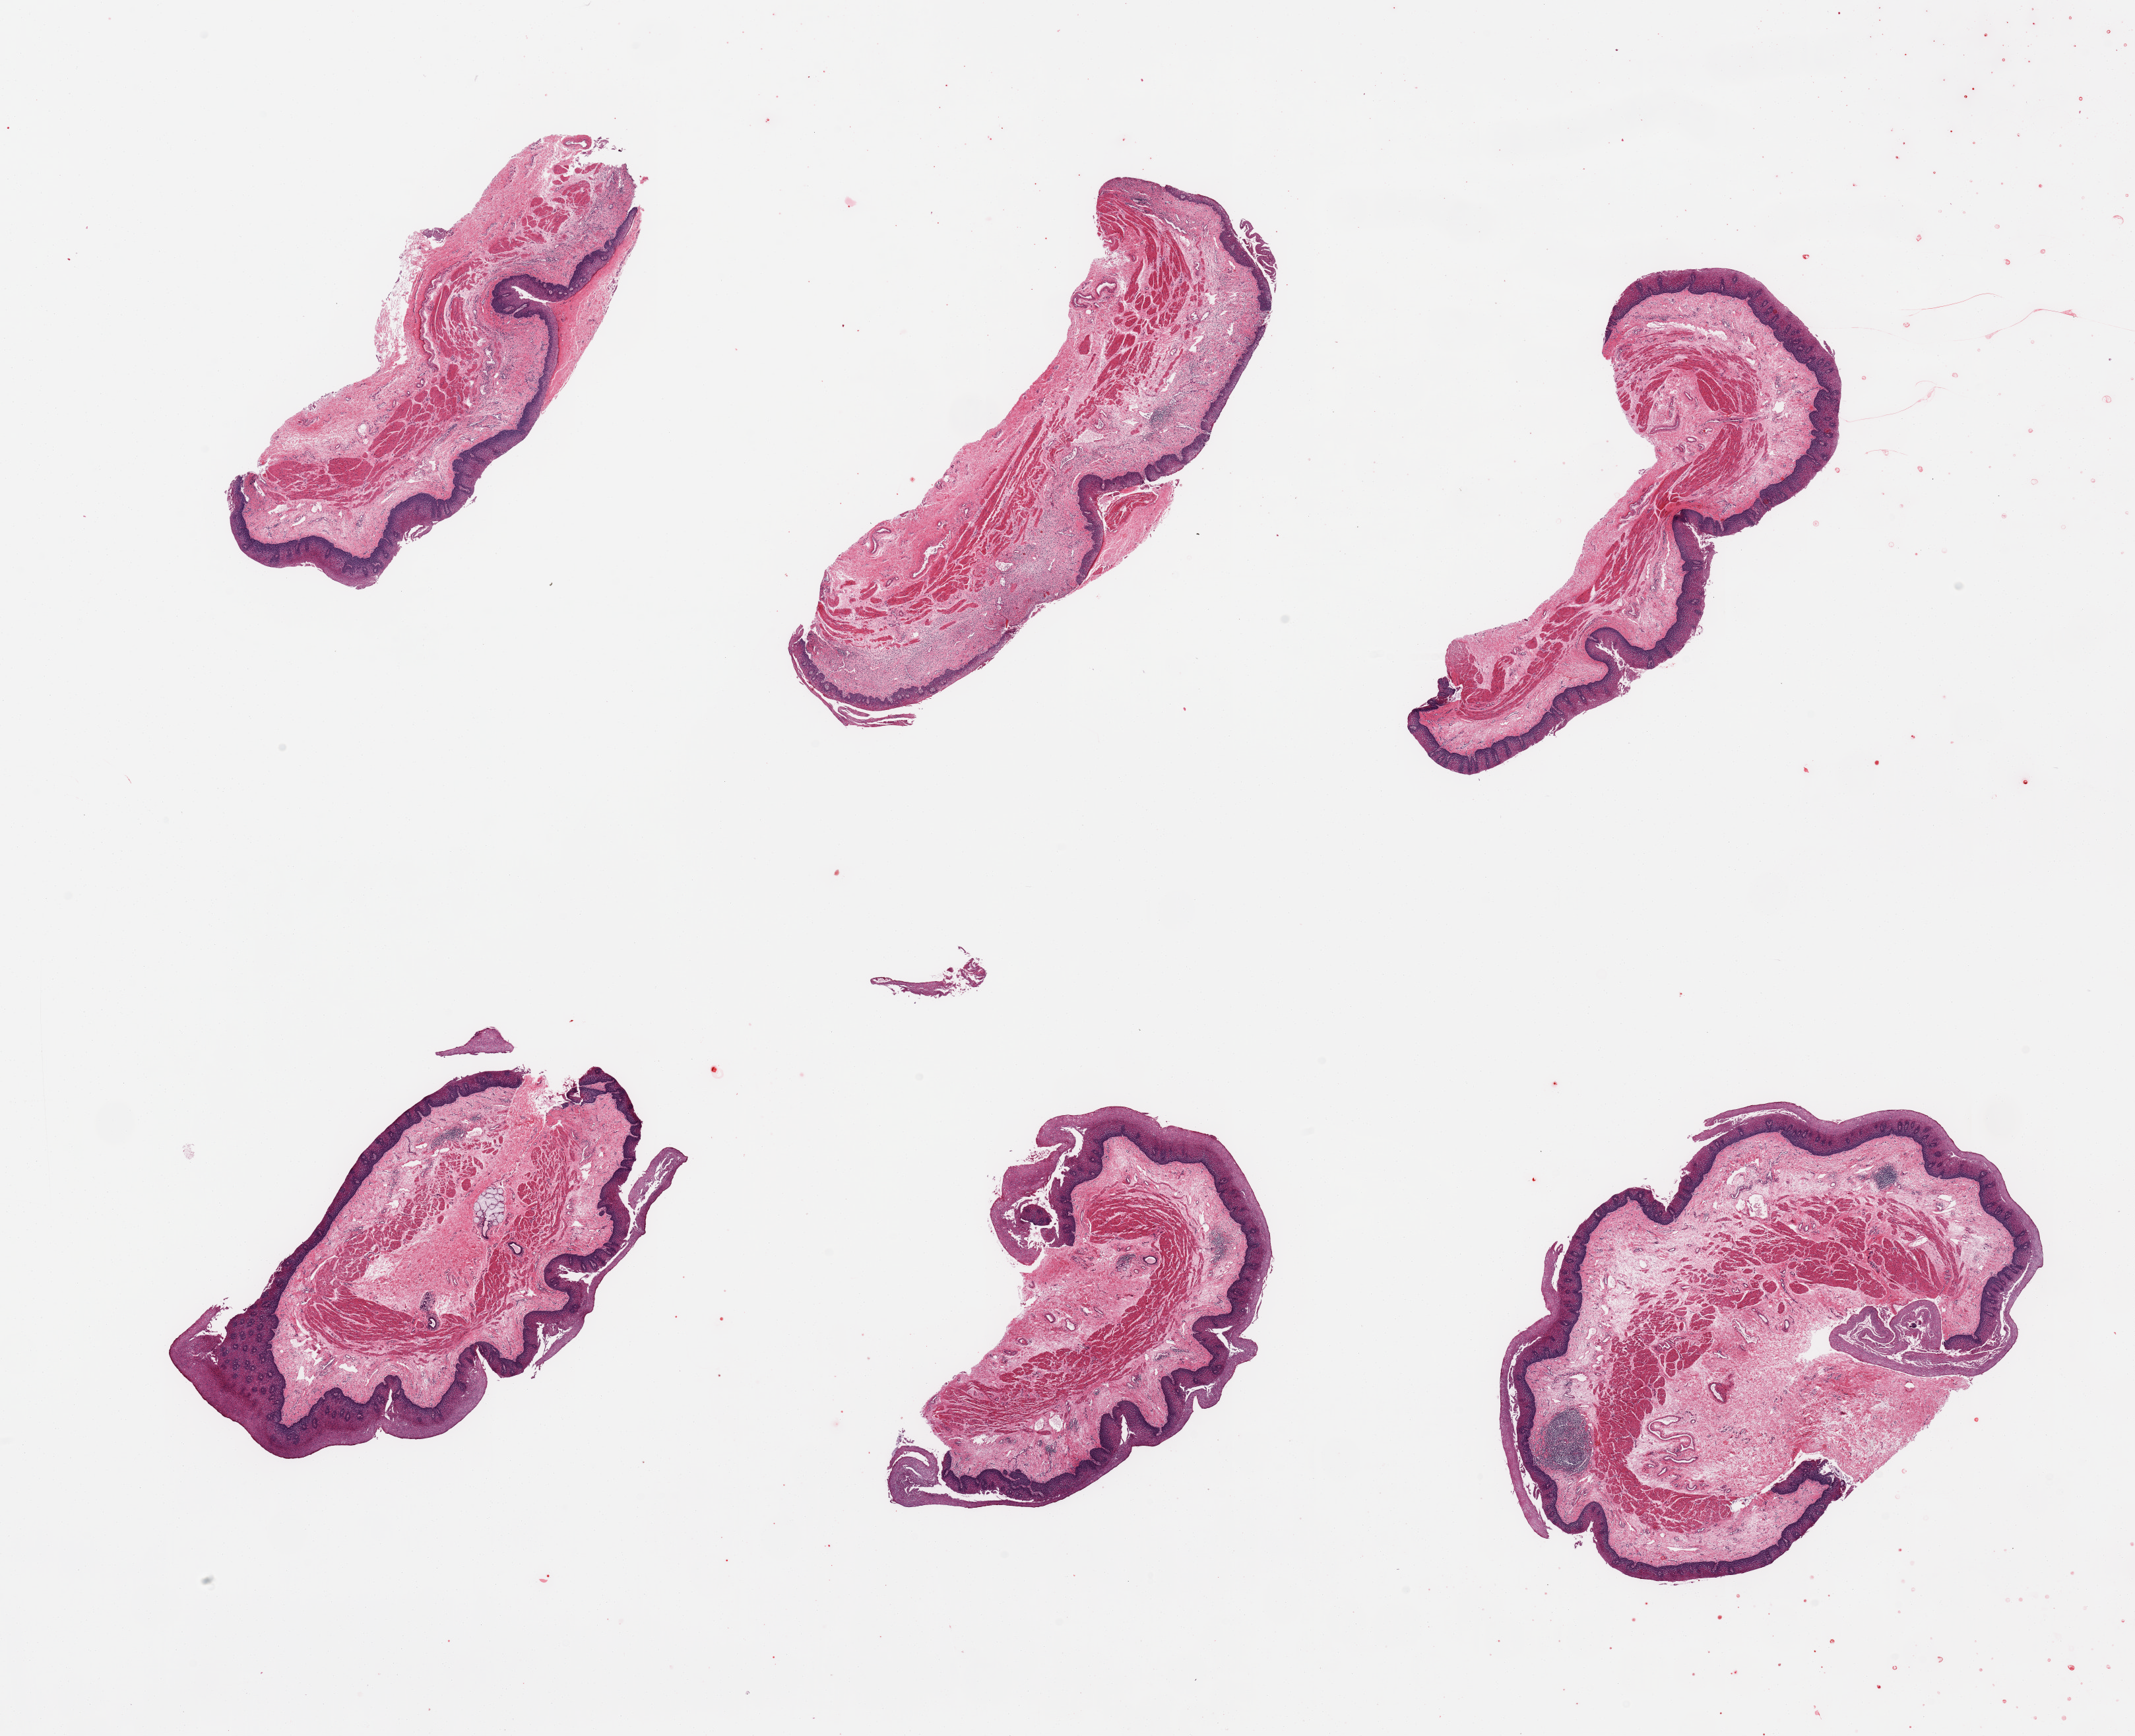
Whole-slide image, H&E stain — low-resolution overview of the scanned area, about 25.6 x 20.8 mm. PAXgene-fixed, paraffin-embedded tissue. Target tissue: esophageal mucous membrane. Donor tissue sample. Male donor.
* review note (as recorded): 6 pieces; foci of chronic inflammation in lamina propria